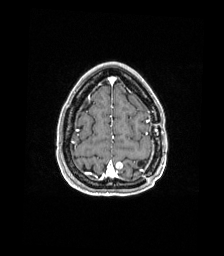
Brain MRI from a brain-tumour surgery series, one axial slice. Position 39 of 176 along the scan axis. T1-weighted post-contrast. 224 × 256 image matrix, field of view 224 × 256 mm. From the clinical record (not read from this slice): histopathology: Atypical meningioma; WHO grade: 2.
Outlined on this slice (outlined manually by an expert reader):
- previous resection cavity: box from (x=138, y=160) to (x=146, y=167) px
- tumour: (x=115, y=162)–(x=123, y=170)